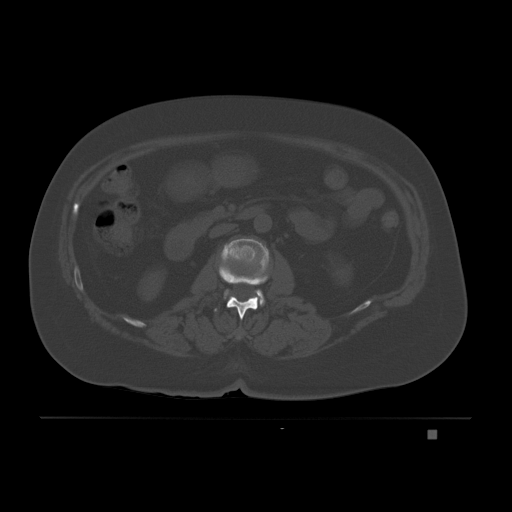
CT including the spine, one axial slice. Position 68 of 221 along the scan axis. Bone window (W 1800 / L 400 HU). 3 mm slice thickness. 512 × 512 image matrix. Female patient, age 63 years. Case-level facts recorded for this patient, not image findings: primary cancer: breast.
Annotated regions visible in this slice (semi-automatically segmented with operator editing):
- L1 vertebra: box from (x=214, y=261) to (x=269, y=320) px
- L2 vertebra: (x=221, y=238)–(x=269, y=306)
- T12 vertebra: (x=238, y=336)–(x=241, y=338)